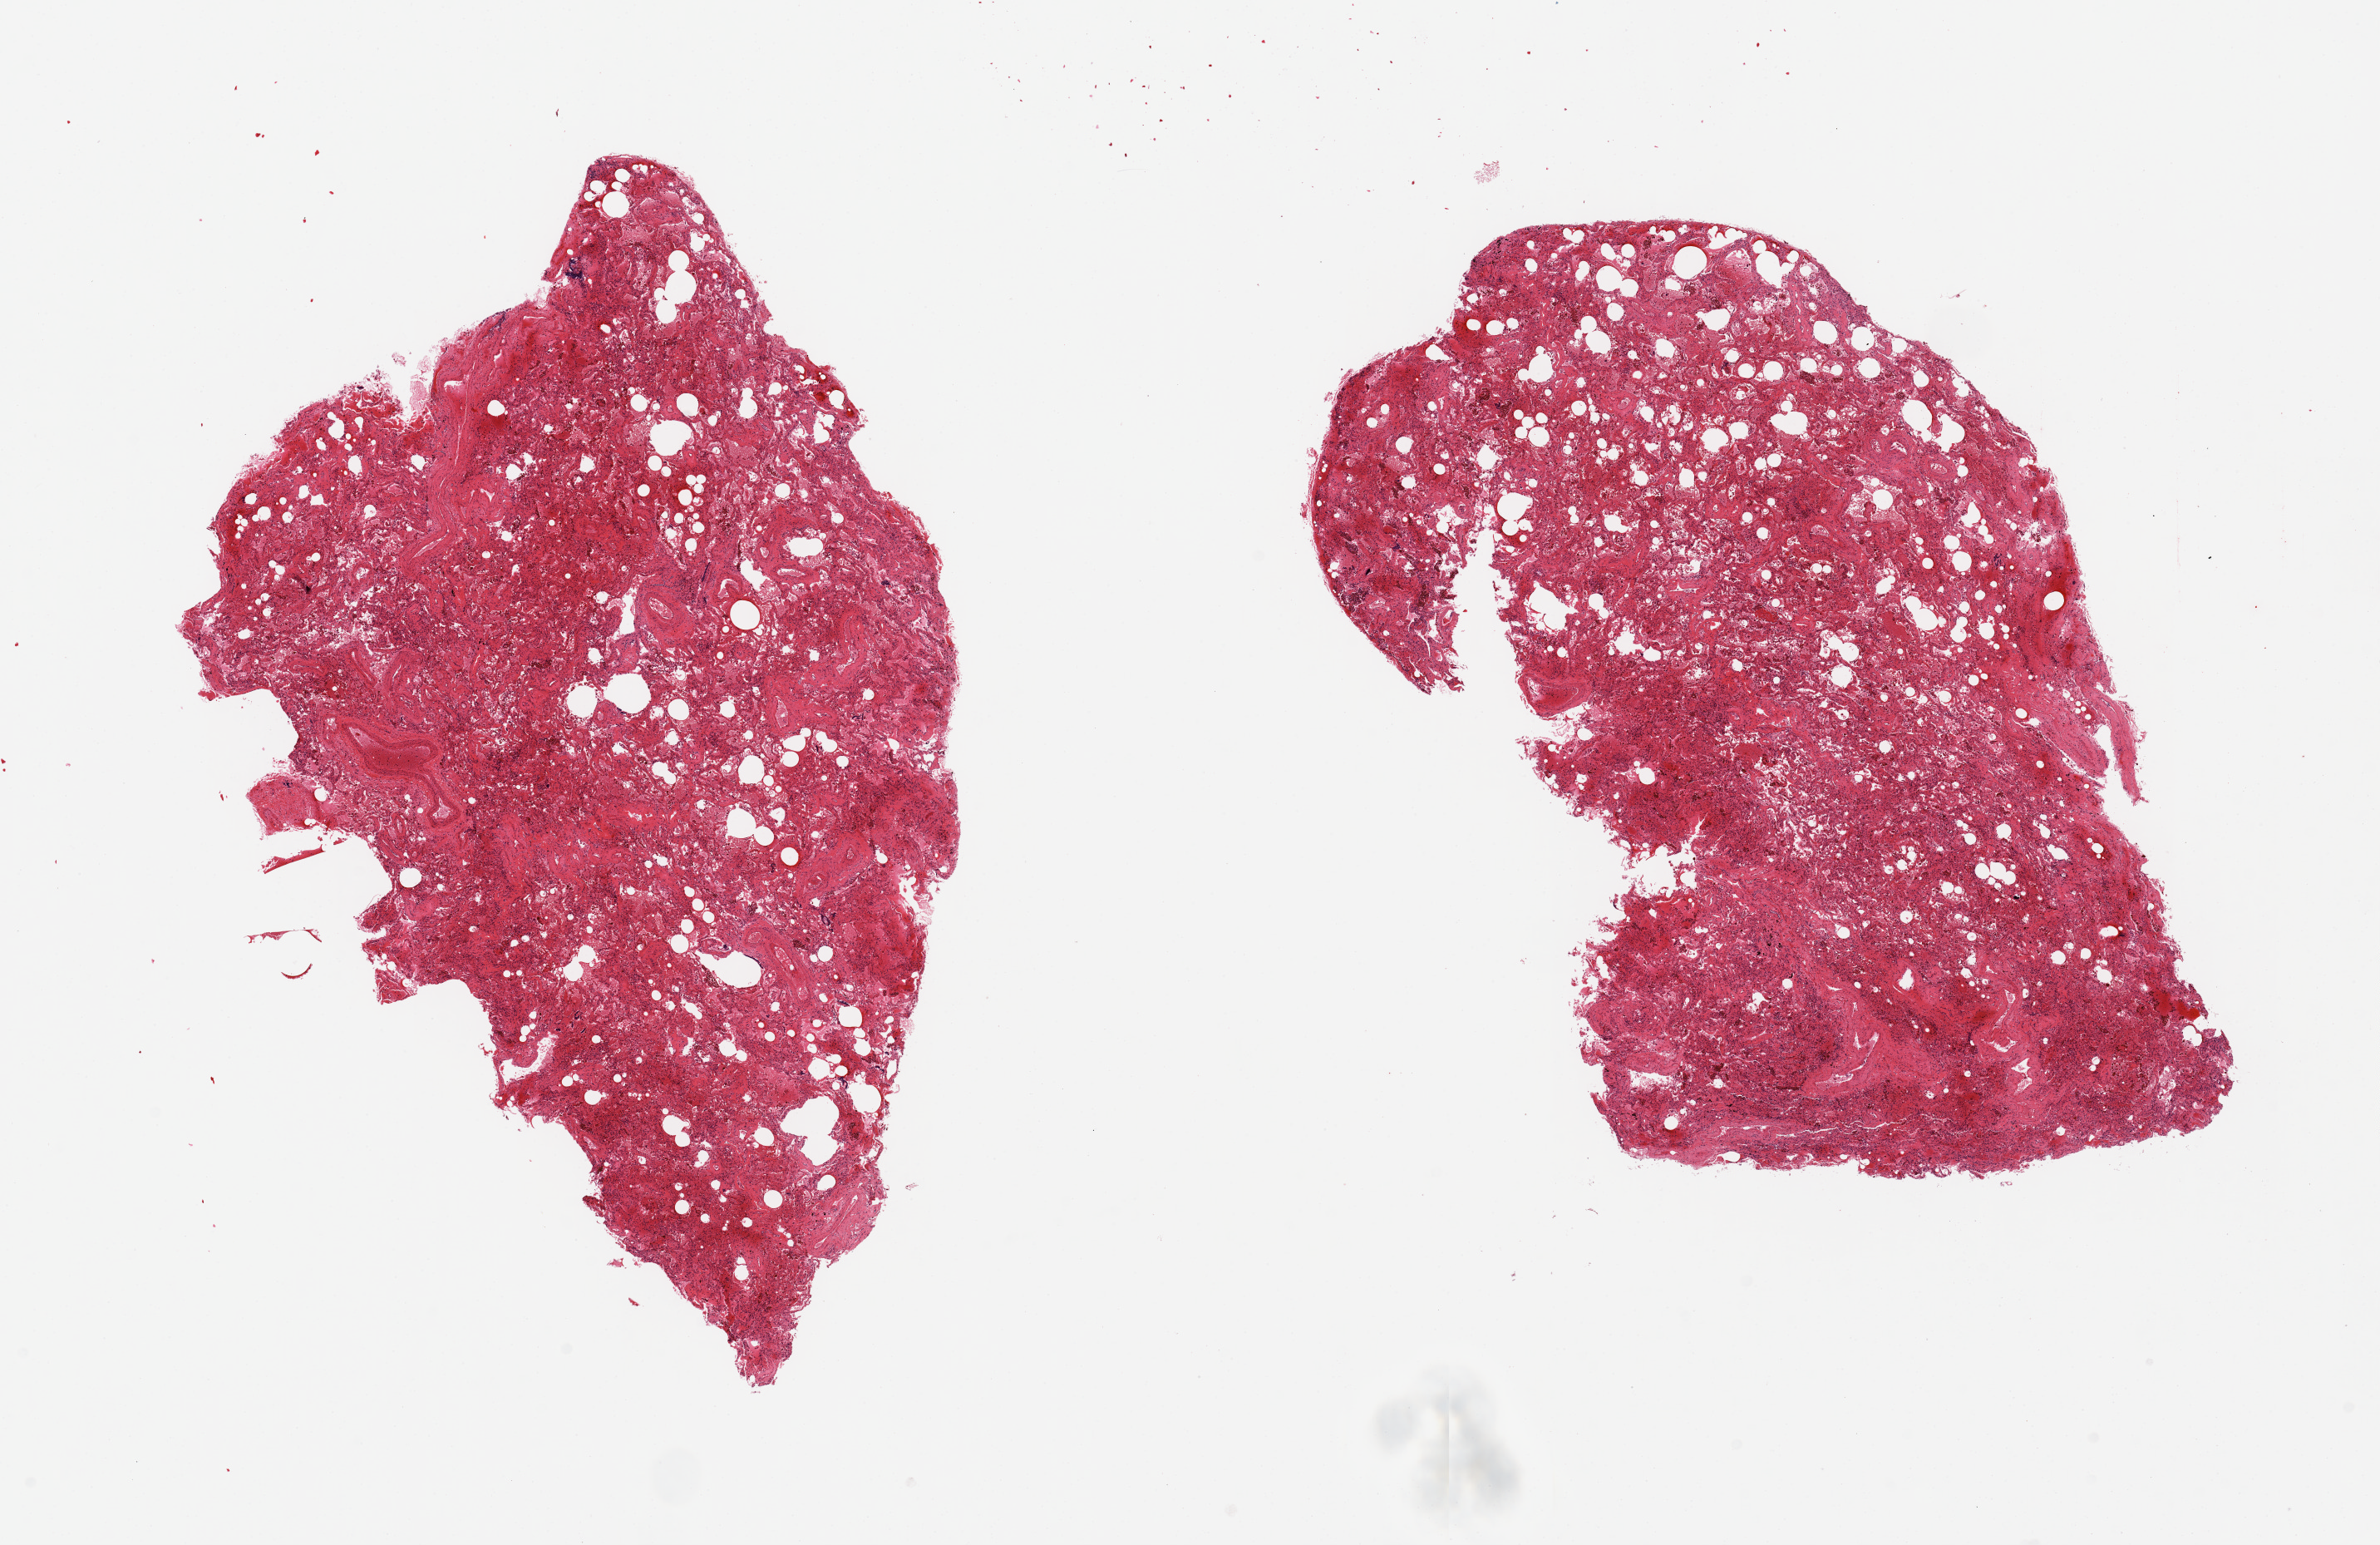
Hematoxylin and eosin (H&E) whole-slide image — a low-resolution overview of the entire scanned area, about 22.6 x 14.7 mm (slide scanned at 20x). PAXgene-fixed, paraffin-embedded tissue. Target tissue: lung. Donor tissue sample. Female donor.
Reviewer comment on this tissue sample: 2 pieces; severe alveolar hemorrhage and numerous heart failure cells; thick walled vessels.